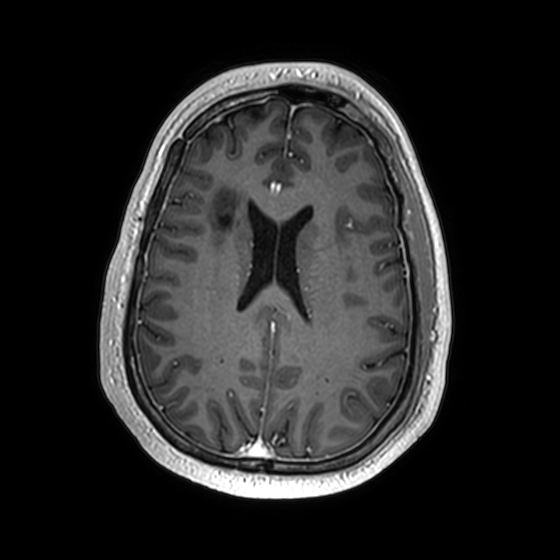
Brain MRI from a brain-tumour surgery series, one axial slice. Slice 70 of 174 in the series (ordered by position). T1-weighted post-contrast. 1 mm slice thickness. 560 × 560 image matrix. Case-level facts recorded for this patient, not image findings: histopathology: Astrocytoma; WHO grade: 2; IDH mutation: yes.
Structures marked on this image (expert manual segmentation):
- previous resection cavity: box from (x=221, y=217) to (x=228, y=225) px